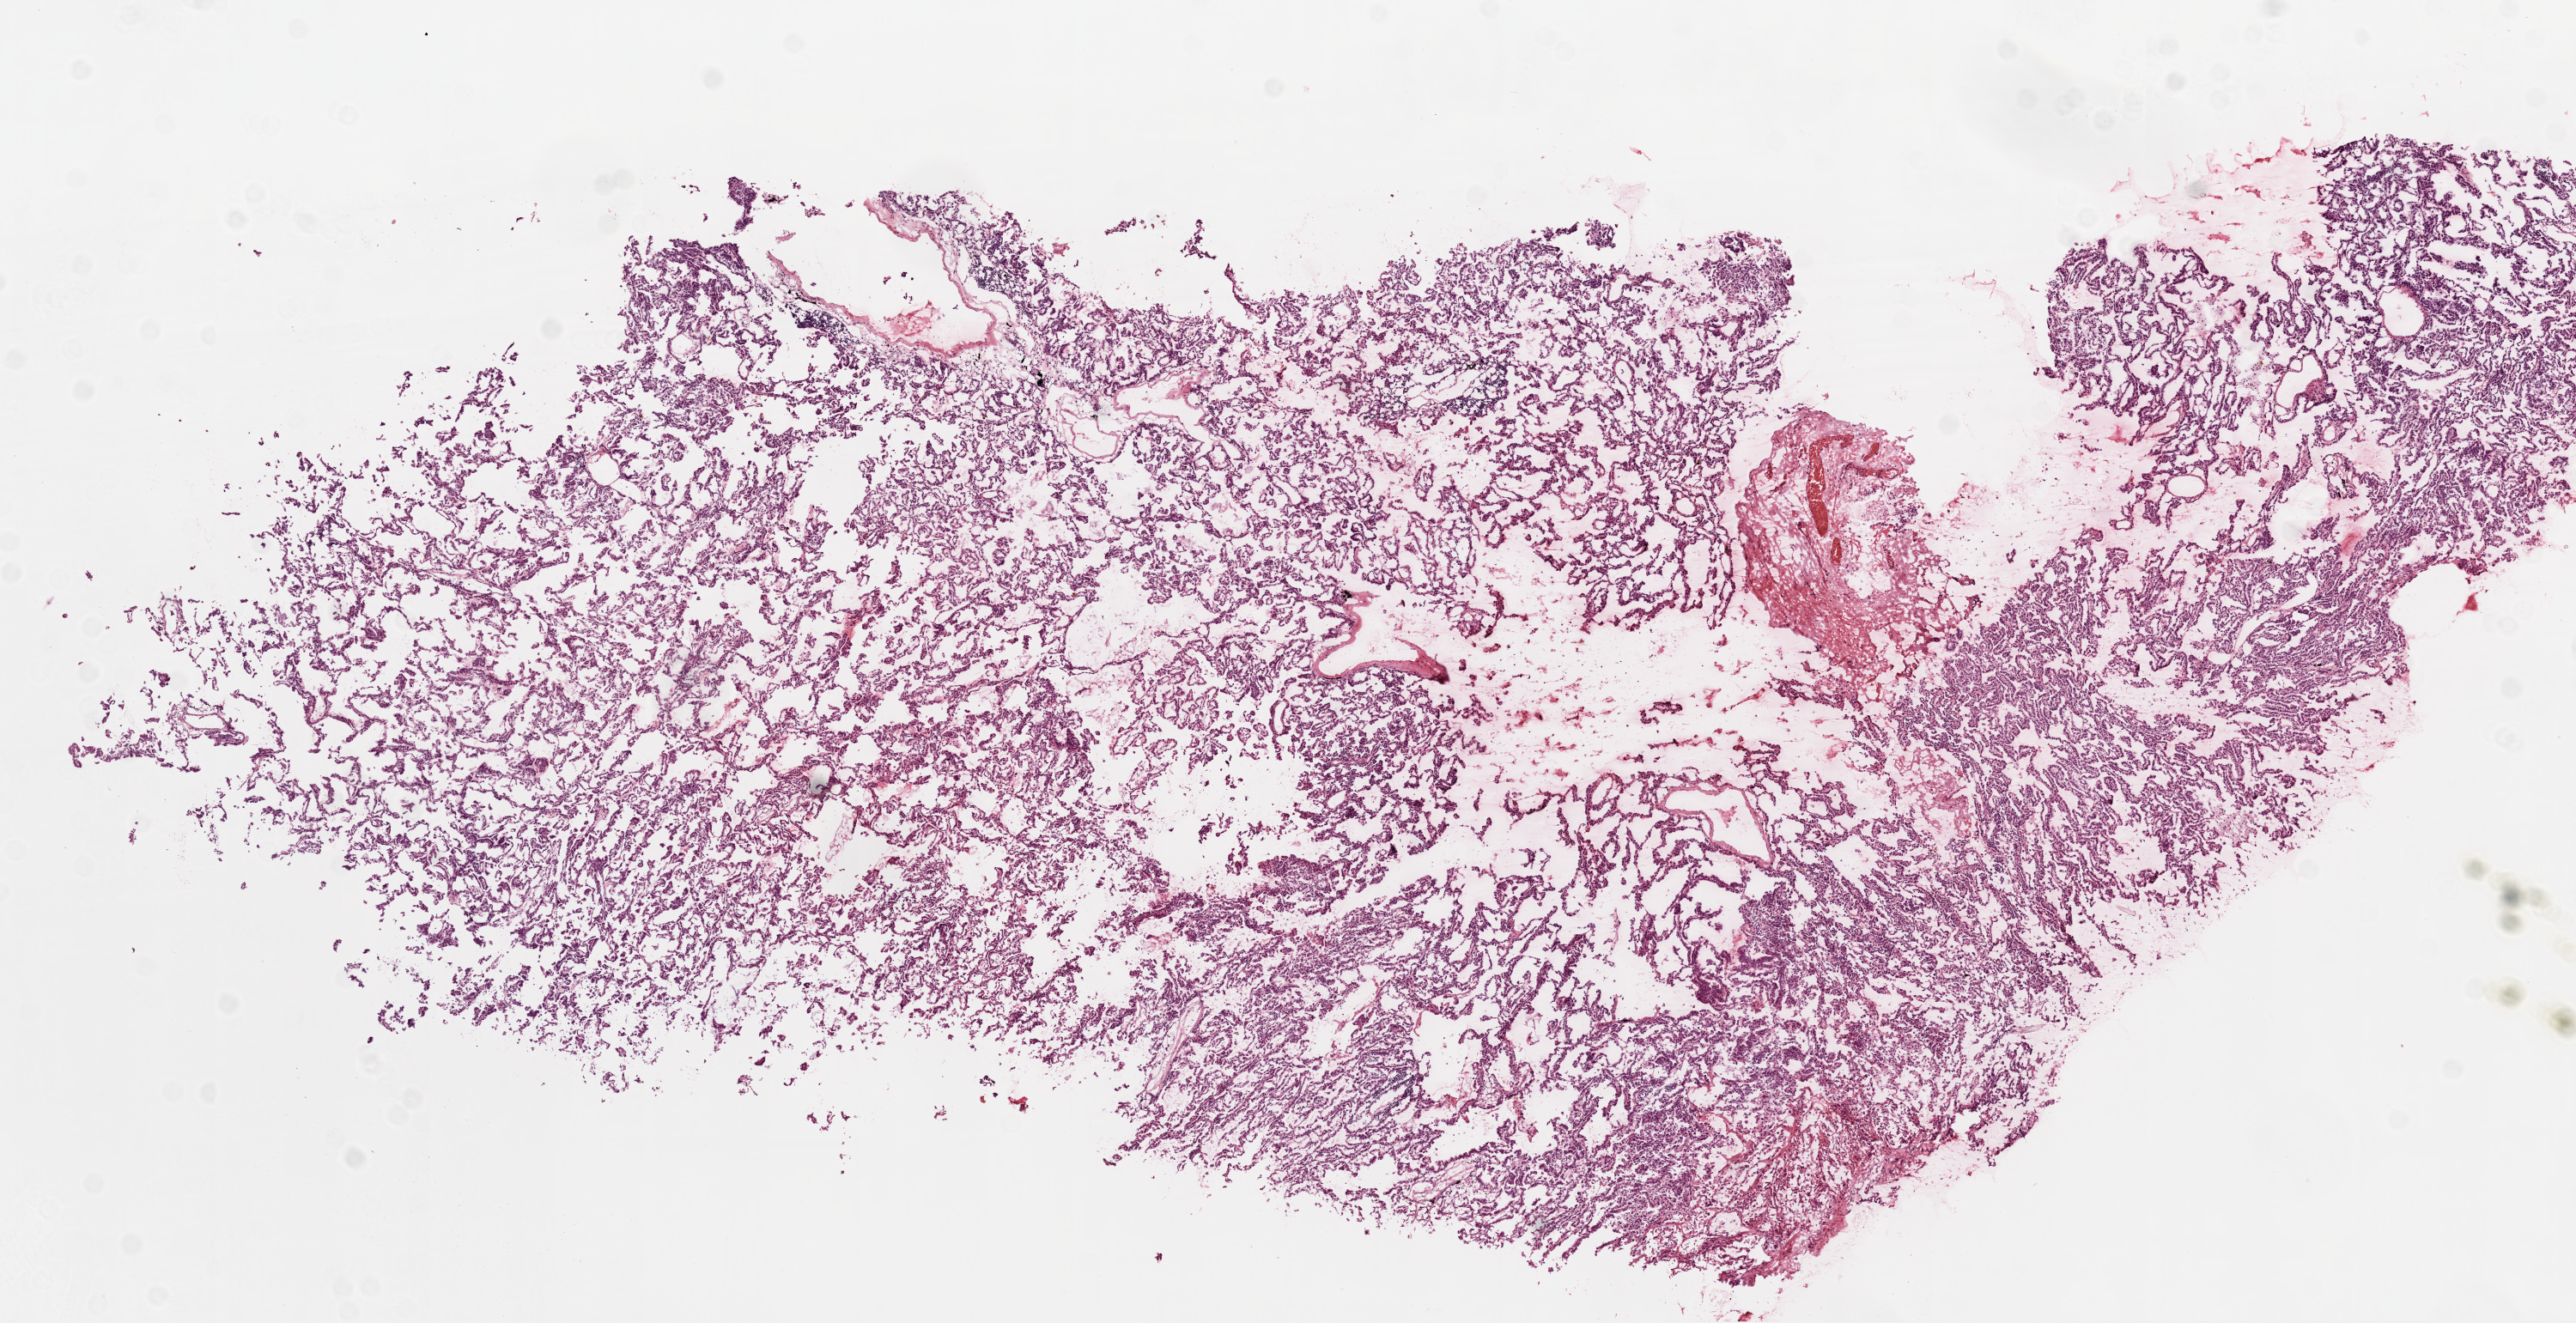
Digitized Hematoxylin and eosin (H&E) stained tissue section (whole slide) — low-resolution overview of the scanned area, about 12.0 x 6.2 mm (slide scanned at 20x); frozen section from the top of the tissue portion; primary tumour sample from the lung. Male patient; age at initial diagnosis 72 years. Composition of this section per pathologist review: tumour cells 94%, tumour nuclei 75%, normal cells 0%, stromal cells 5%, necrosis 1%.
- pathologic diagnosis: Adenocarcinoma, NOS (lower lobe, lung)
- AJCC pathologic stage: IA (3rd edition)